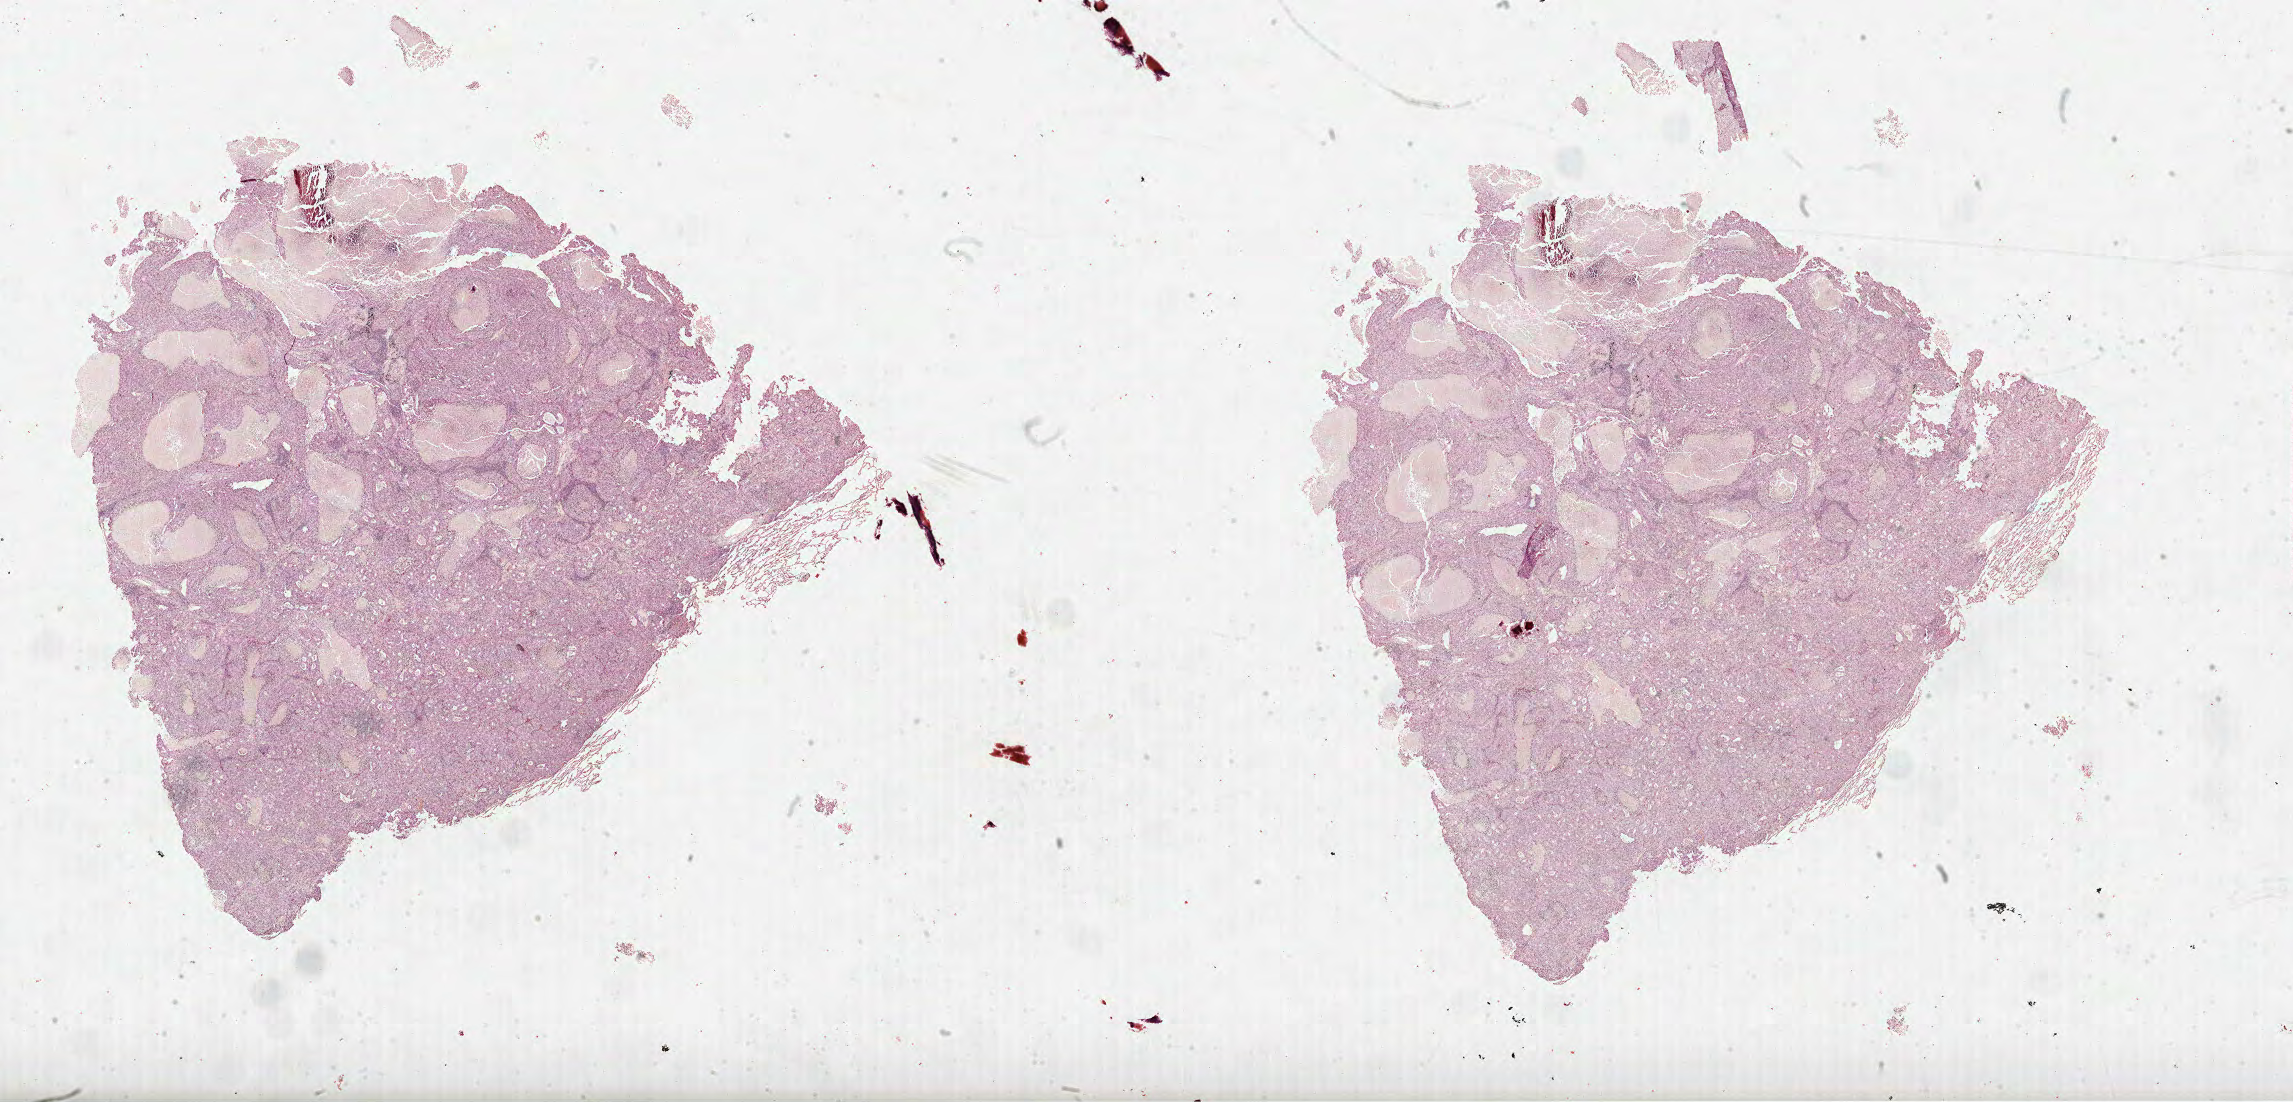
H&E-stained whole-slide image — shown as a low-resolution overview of the whole scanned area (about 37.0 x 17.8 mm); FFPE section; sample: primary tumour, lung. Male, age 55 years at initial diagnosis.
• diagnosis: Adenocarcinoma, NOS (upper lobe, lung)
• TNM: T2 N1 M0
• AJCC pathologic stage: IIB